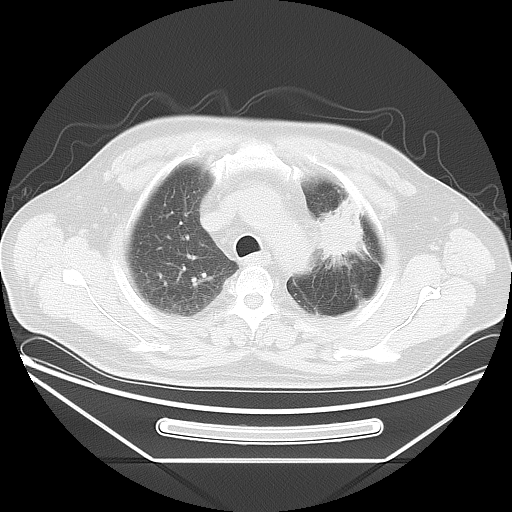
Chest CT, one axial slice. Position 31 of 37 along the scan axis. Lung window (W 1500 / L -600 HU). 512 × 512 image matrix. Patient: male, 61 years. From the clinical record (not read from this slice): clinical TNM (as recorded): T2a N0 M0; histopathological grade: G3.
Structures marked on this image (rectangle marked by the reading radiologist):
- lung tumour (recorded histology: small cell carcinoma): bounding box <315,186,382,271> (left, top, right, bottom; pixels)